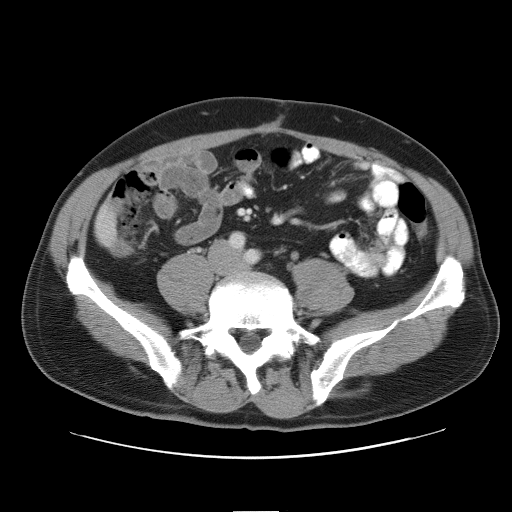
Contrast-enhanced abdominal CT, one axial slice. Slice 7 of 52 in the series (ordered by position). Intravenous contrast given. Soft-tissue window (W 400 / L 40 HU). 5 mm slice thickness. 512 × 512 image matrix. Male patient, age 70 years. From the clinical record (not read from this slice): diagnosis: colorectal cancer liver metastases, imaged before liver resection; multiple liver metastases: yes; largest metastasis: 4 cm; chemotherapy before resection: yes.
Annotated regions visible in this slice (manually delineated by an expert):
- liver: box from (x=96, y=209) to (x=116, y=245) px